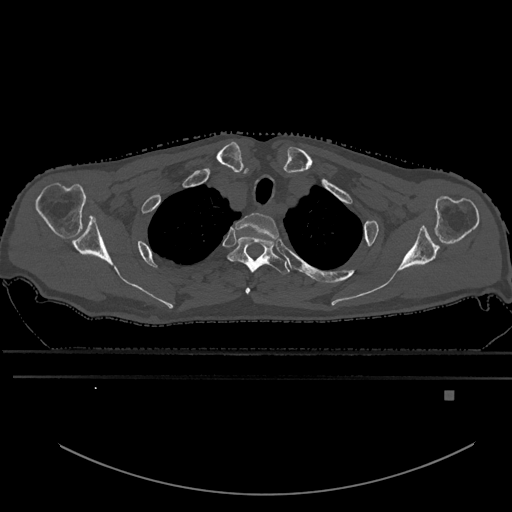
CT including the spine, one axial slice. Slice 504 of 969 in the series (ordered by position). Bone window (W 1800 / L 400 HU). 512 × 512 image matrix, field of view 456 × 456 mm. Male patient, age 82 years. From the clinical record (not read from this slice): primary cancer: prostate; vertebrae with lytic lesions (as recorded): T11, T9, T8, T2.
Structures marked on this image (semi-automatically segmented with operator editing):
- T1 vertebra: bounding box (x1, y1, x2, y2) in pixels: (236, 212, 279, 291)
- T2 vertebra: (228, 237, 290, 294)